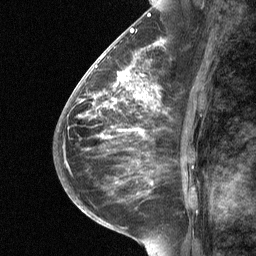
Breast MRI (dynamic contrast-enhanced), one sagittal slice. Position 34 of 64 along the scan axis. Dynamic contrast-enhanced study with each time point stored as its own series, time point 2 of 3 at this slice position (early post-contrast, ordered by acquisition time). 1.5 T. TE 4.8 ms, TR 27 ms. 2 mm slice thickness. 256 × 256 image matrix, field of view 180 × 180 mm. Female patient, age 59 years. From the clinical record (not read from this slice): setting: breast cancer imaged before/during neoadjuvant chemotherapy; receptor status: triple-negative.
Annotated regions visible in this slice (semi-automatically segmented with operator editing):
- analysis volume of interest (the breast-tissue region the enhancement analysis was run in; not a lesion): box from (x=113, y=66) to (x=159, y=112) px
- tumour enhancement mask (voxels above the 90 % enhancement threshold inside the analysis volume of interest): (x=118, y=71)–(x=149, y=103)